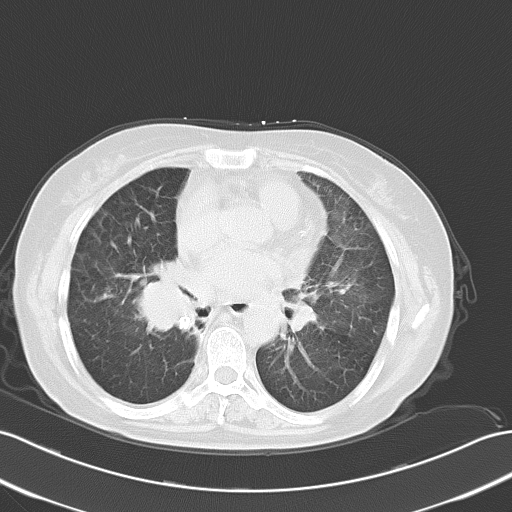
Chest CT, one axial slice; slice 33 of 62 in the series (ordered by position); reconstruction kernel B70f; 120 kVp; lung window (W 1500 / L -600 HU); 5 mm slice thickness; 512 × 512 image matrix, field of view 353 × 353 mm. Patient: female, 65 years. From the clinical record (not read from this slice): clinical TNM (as recorded): T1c N3 M0; histopathological grade: G3.
Annotated regions visible in this slice (rectangle marked by the reading radiologist):
- lung tumour (recorded histology: small cell carcinoma): bounding box [x1, y1, x2, y2] px = [131, 259, 208, 342]